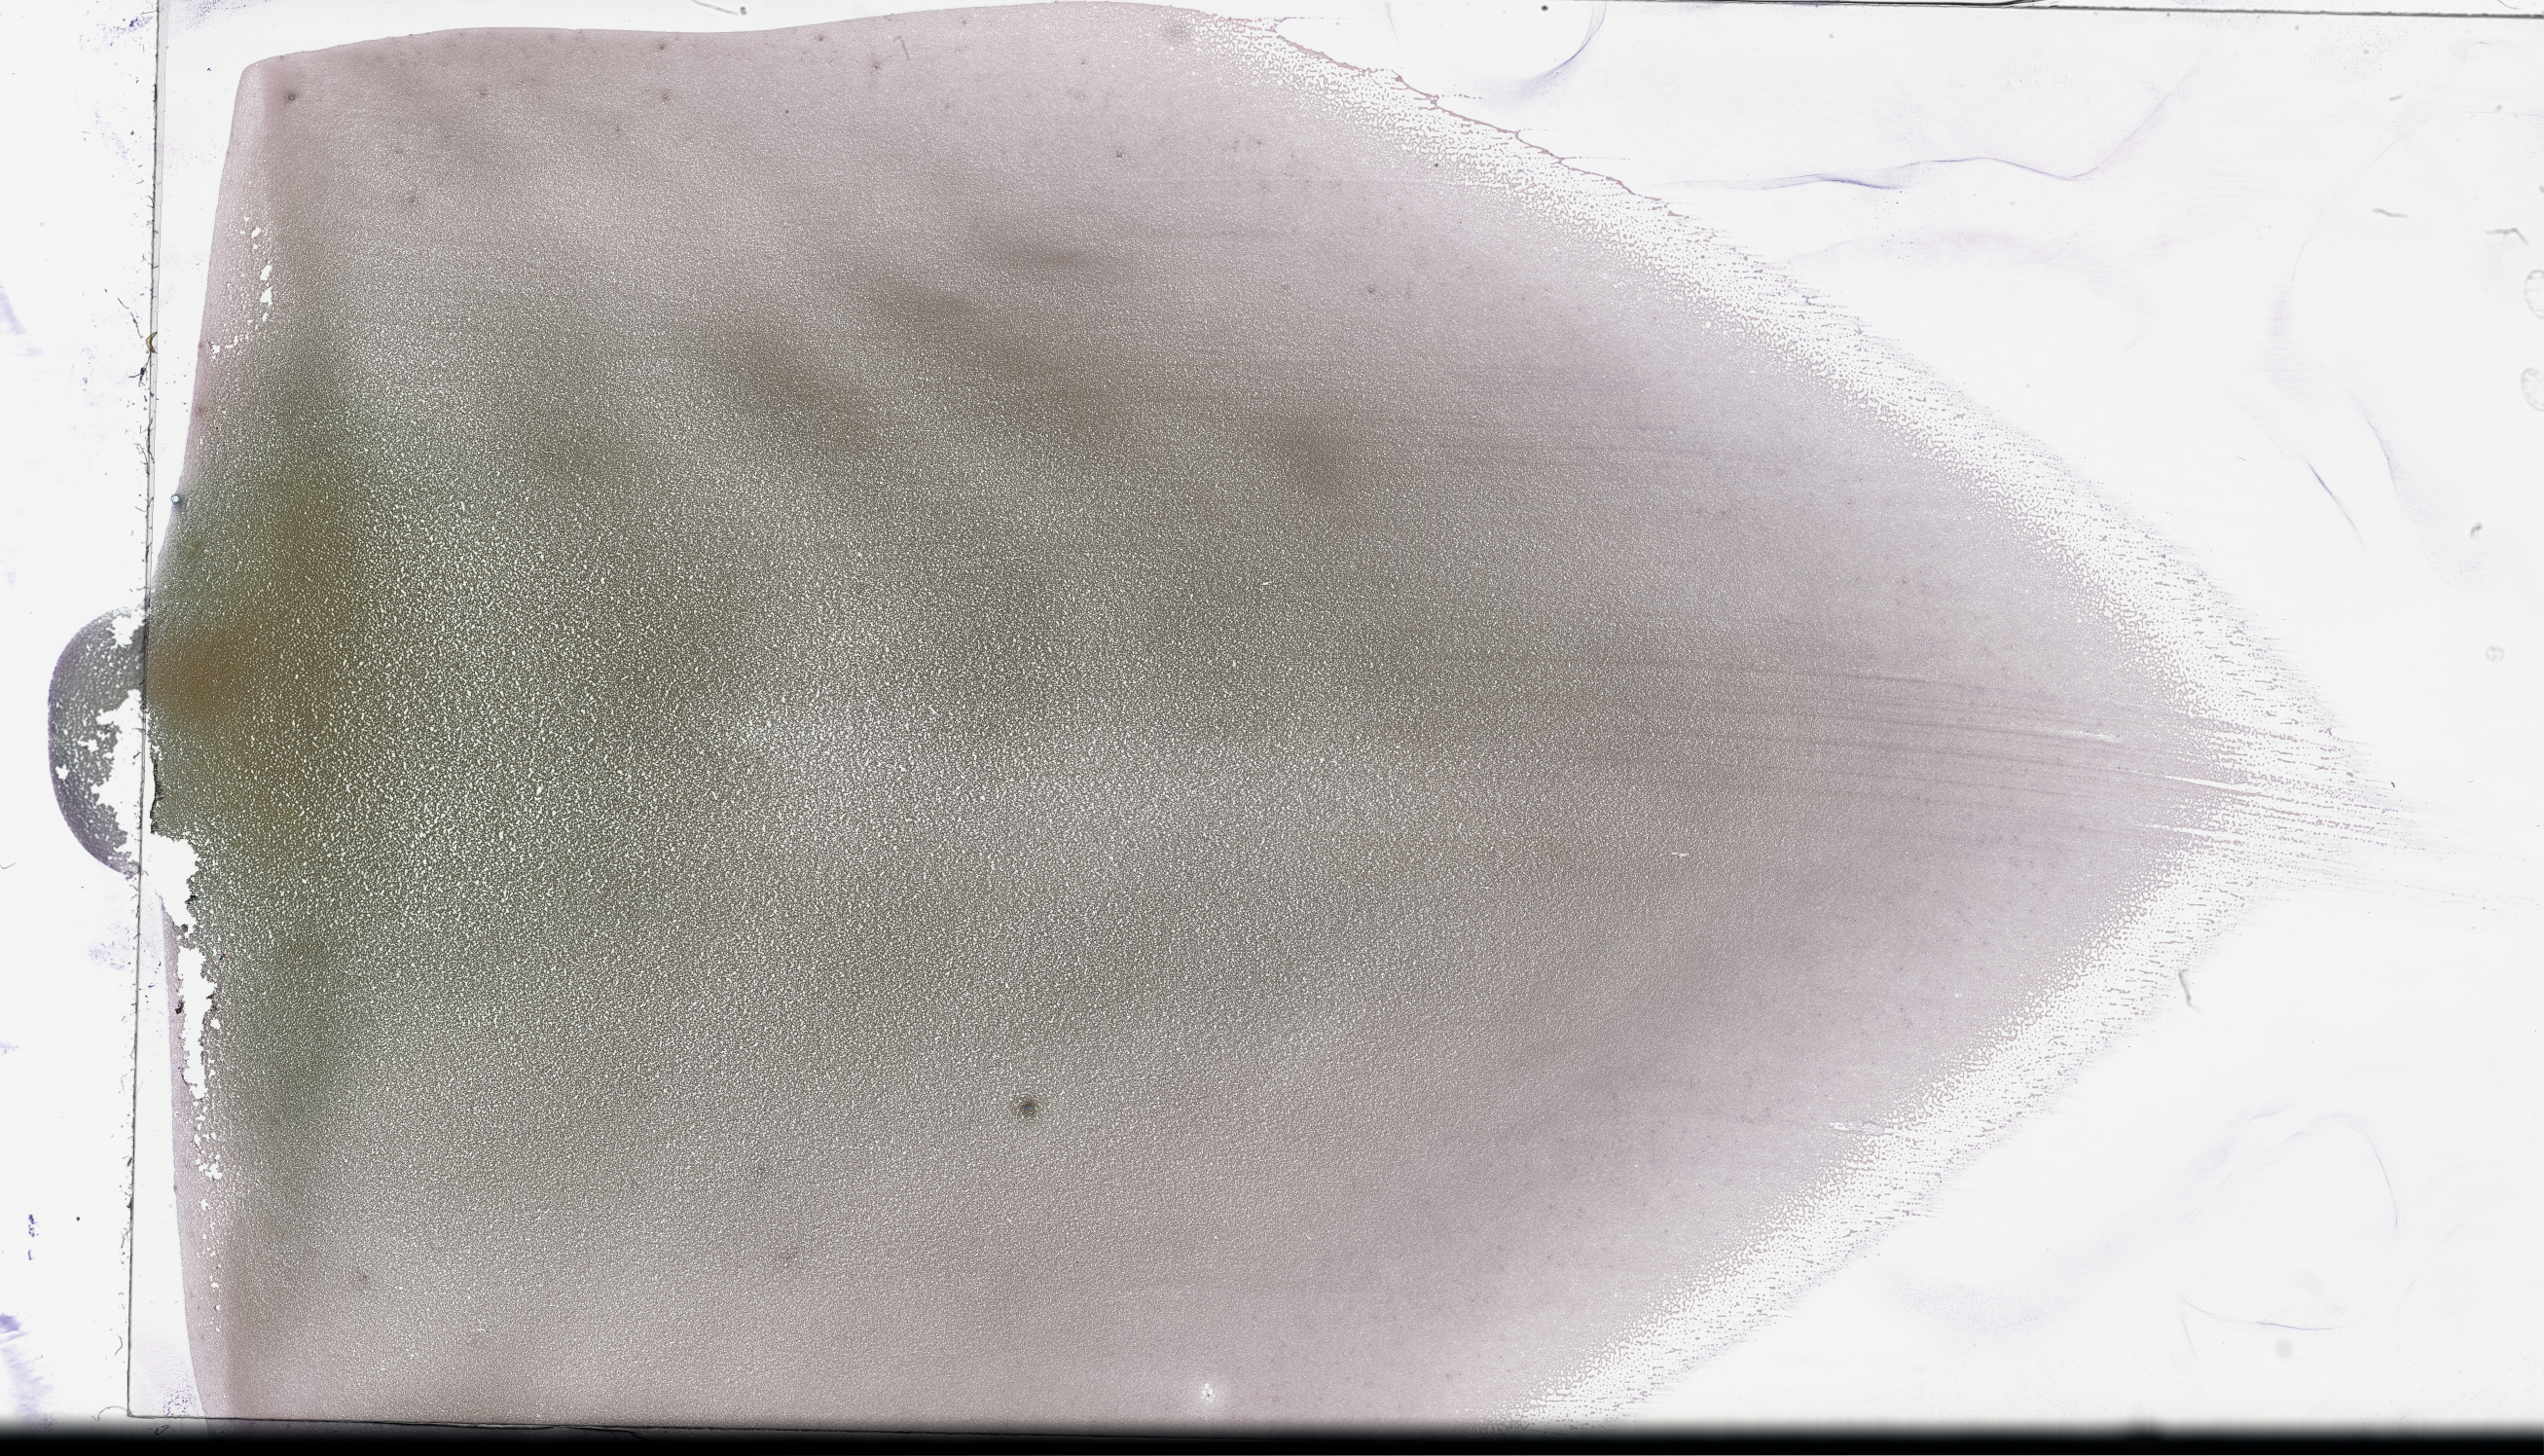
Whole-slide image of a whole blood smear, Wright-Giemsa stain — shown as a low-resolution overview of the whole scanned area (about 42.2 x 24.2 mm), EDTA-anticoagulated smear, collected on treatment. Patient sex: male.
• from a patient with: Plasma Cell Myeloma